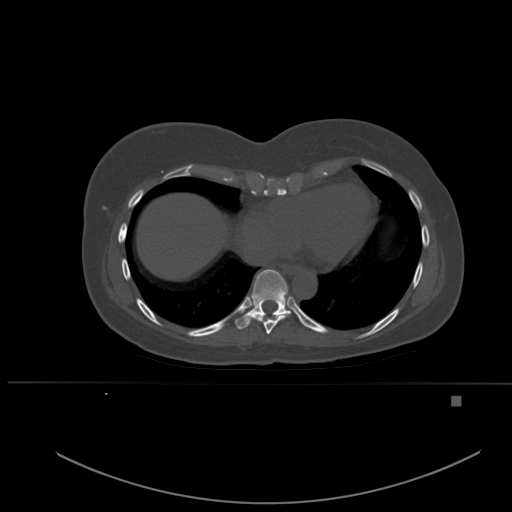
CT including the spine, one axial slice; position 312 of 651 along the scan axis; bone window (W 1800 / L 400 HU); 1.5 mm slice thickness; 512 × 512 image matrix, field of view 443 × 443 mm. Patient: female, 49 years. Case-level facts recorded for this patient, not image findings: primary cancer: breast.
Annotated regions visible in this slice (semi-automatically segmented with operator editing):
- T8 vertebra: box from (x=252, y=315) to (x=289, y=334) px
- T9 vertebra: (x=227, y=269)–(x=291, y=329)